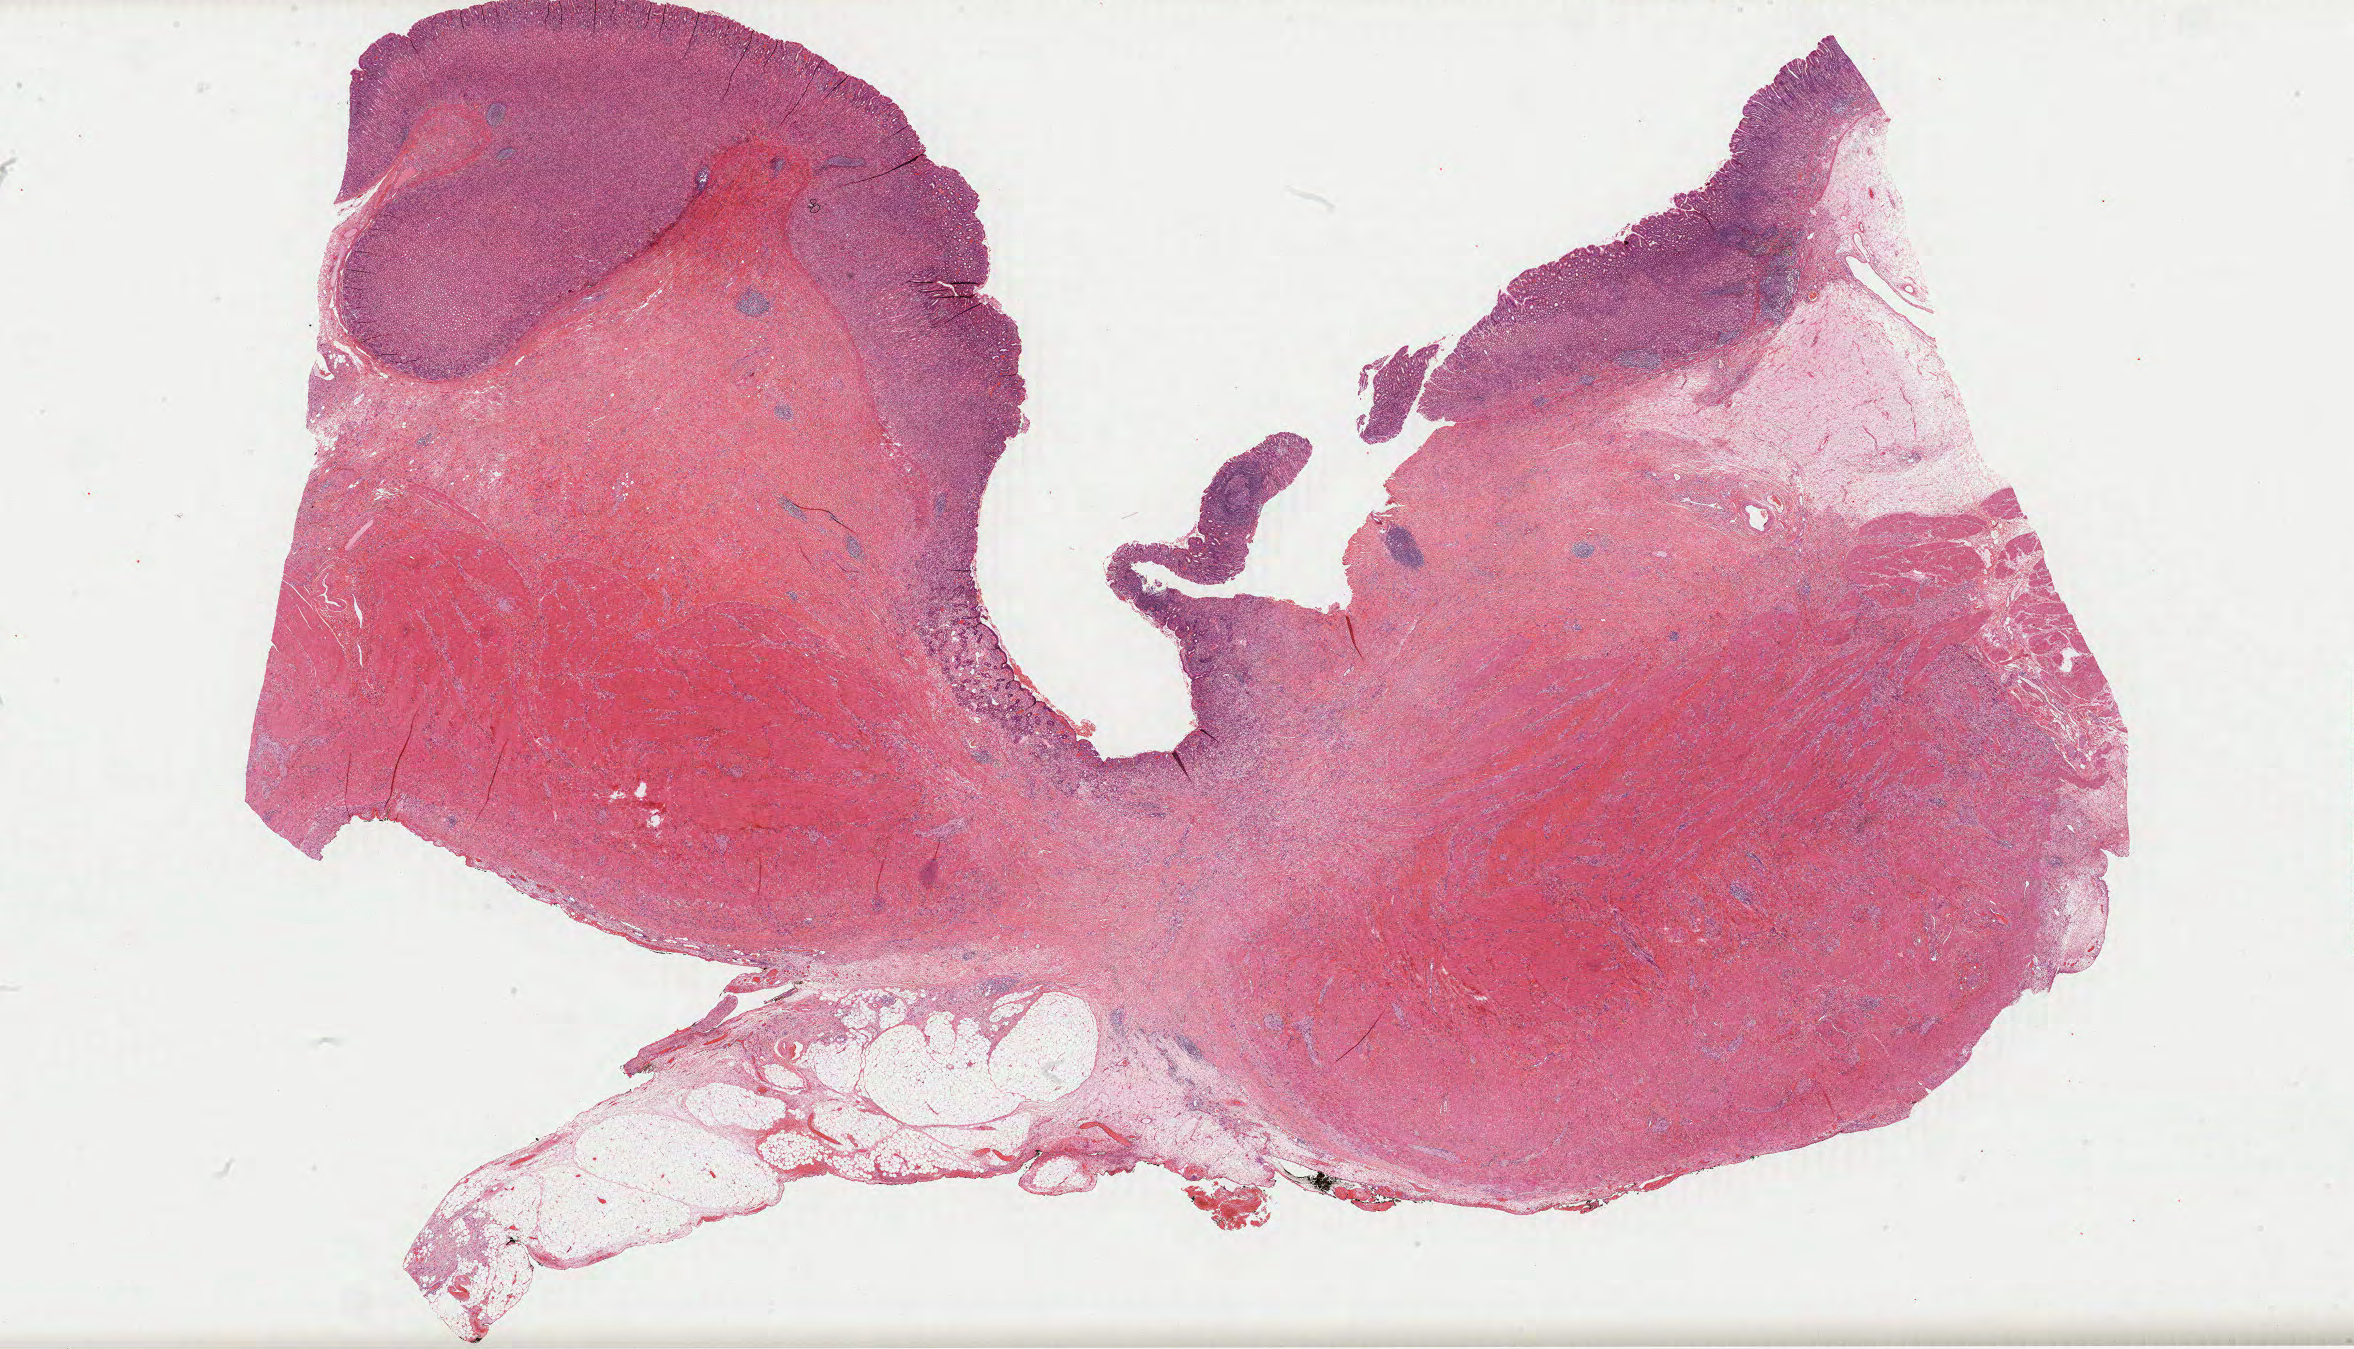
Whole-slide histology image, H&E, shown as a low-resolution overview of the whole scanned area (about 37.8 x 21.7 mm); formalin-fixed paraffin-embedded (FFPE) diagnostic section; stomach, primary tumour sample. Female, age 53 years at initial diagnosis.
Histologic diagnosis: Carcinoma, diffuse type (fundus of stomach).